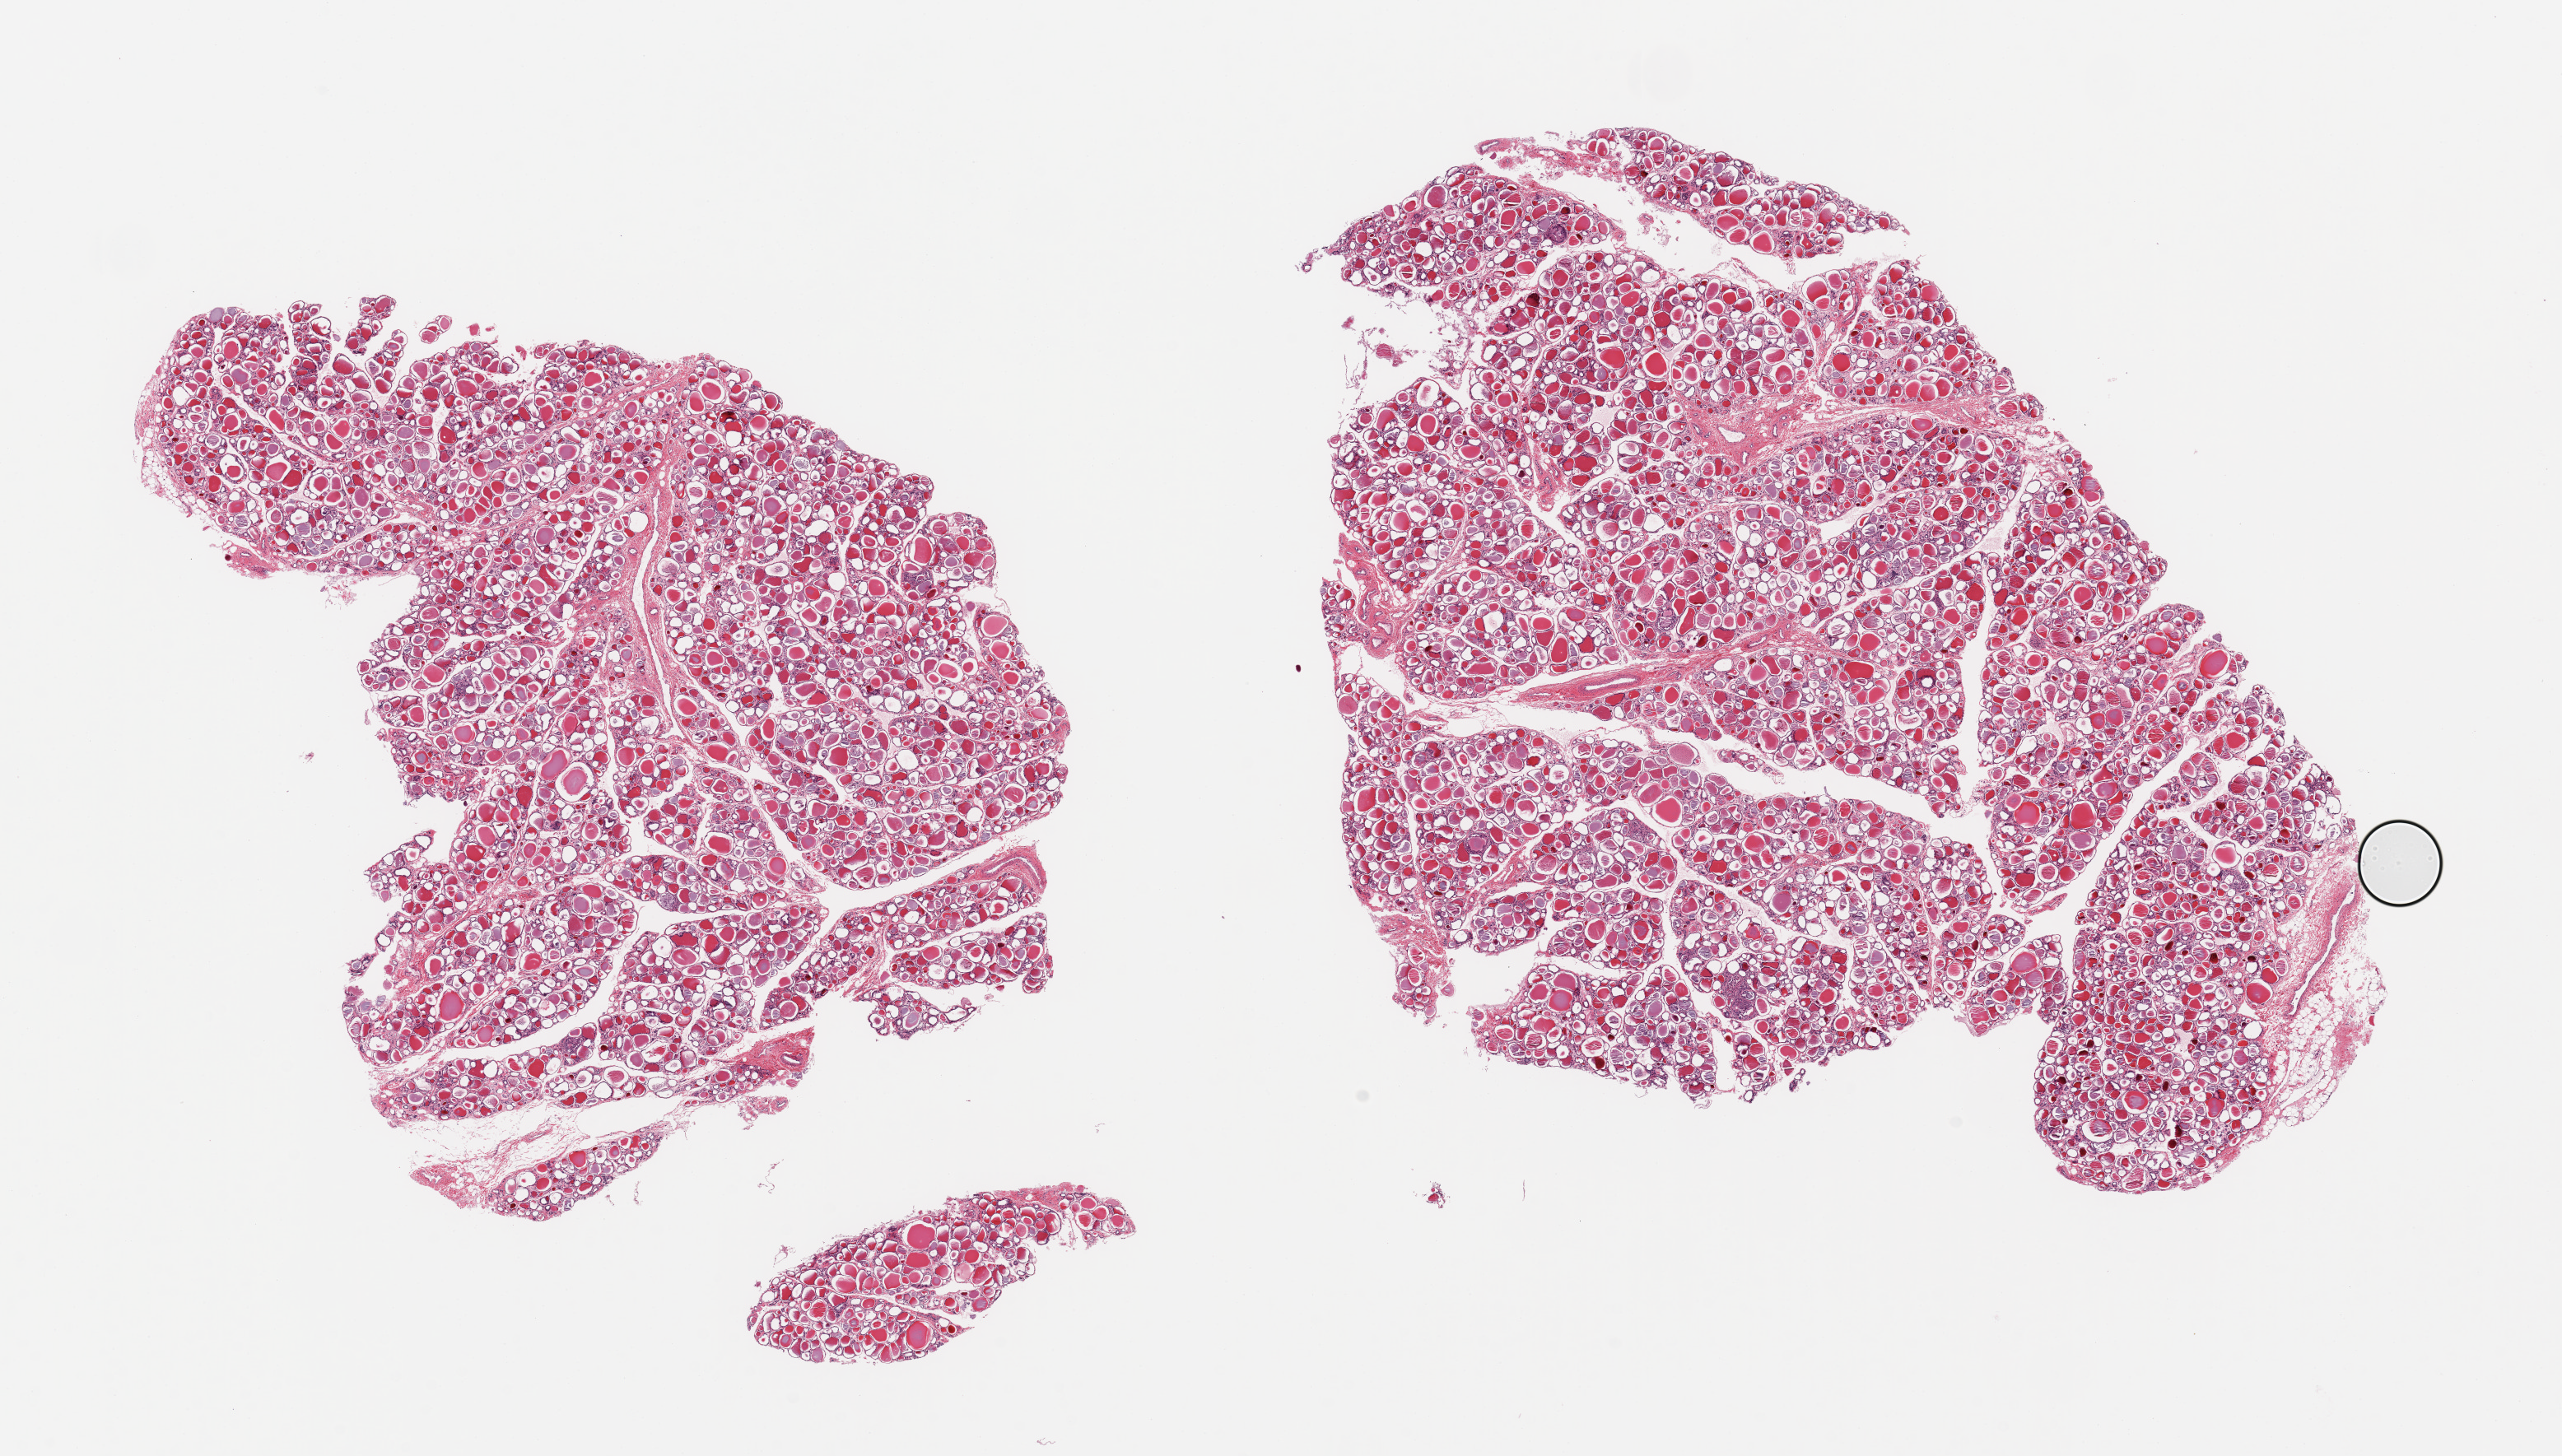
H&E whole-slide image — low-resolution overview of the scanned area, about 24.6 x 14.0 mm (slide scanned at 20x), PAXgene-fixed paraffin-embedded (PFPE) section, target tissue: thyroid, donor tissue sample.
Pathologist's review note for this sample: 2 pieces; trivial amount of attached fat.